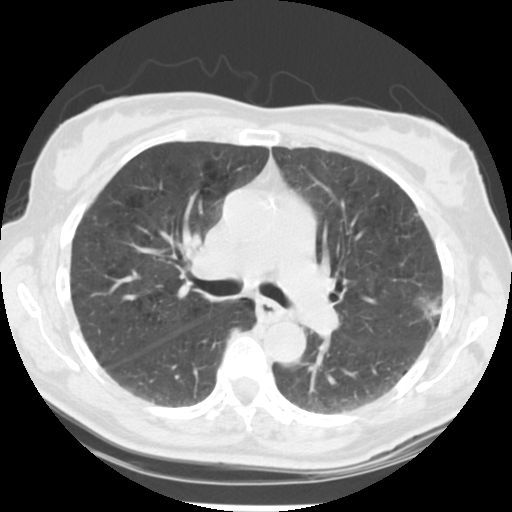
Low-dose screening chest CT, one axial slice. 120 kVp. Lung window (W 1500 / L -600 HU). 2.5 mm slice thickness. 512 × 512 image matrix, field of view 302 × 302 mm.
Structures marked on this image (manually delineated by an expert):
- lesion 1 (tumor, upper lobe of left lung): bounding box (x1, y1, x2, y2) in pixels: (422, 300, 442, 323)